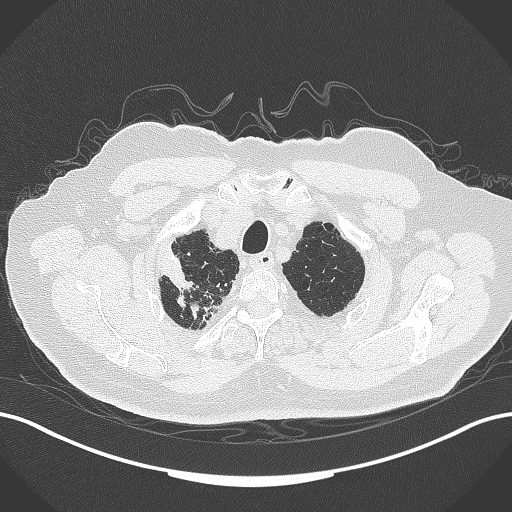
Chest CT, one axial slice; slice 320 of 389 in the series (ordered by position); reconstruction kernel B70f; 120 kVp; lung window (W 1500 / L -600 HU); 1 mm slice thickness; 512 × 512 image matrix, field of view 400 × 400 mm. Patient: male, 72 years. From the clinical record (not read from this slice): clinical TNM (as recorded): T1a N0 M0.
Outlined on this slice (bounding box drawn by a radiologist):
- lung tumour (recorded histology: squamous cell carcinoma): bounding box (x1, y1, x2, y2) in pixels: (158, 243, 196, 293)